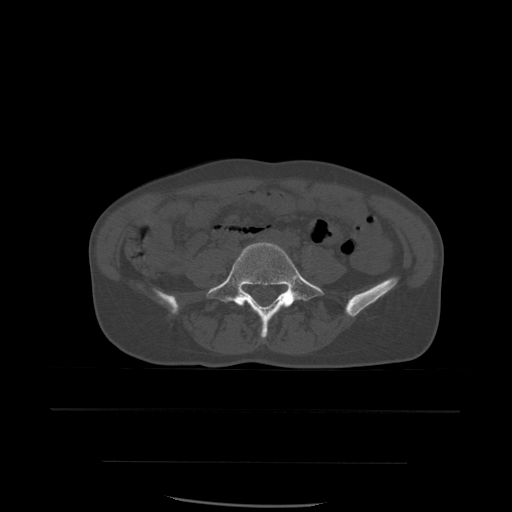
CT including the spine, one axial slice; slice 151 of 574 in the series (ordered by position); bone window (W 1800 / L 400 HU); 1.25 mm slice thickness; 512 × 512 image matrix, field of view 392 × 392 mm. Patient age 48 years. From the clinical record (not read from this slice): primary cancer: lung; vertebrae with lytic lesions (as recorded): T11.
Outlined on this slice (semi-automatically segmented with operator editing):
- L5 vertebra: bounding box [x1, y1, x2, y2] px = [207, 243, 324, 339]